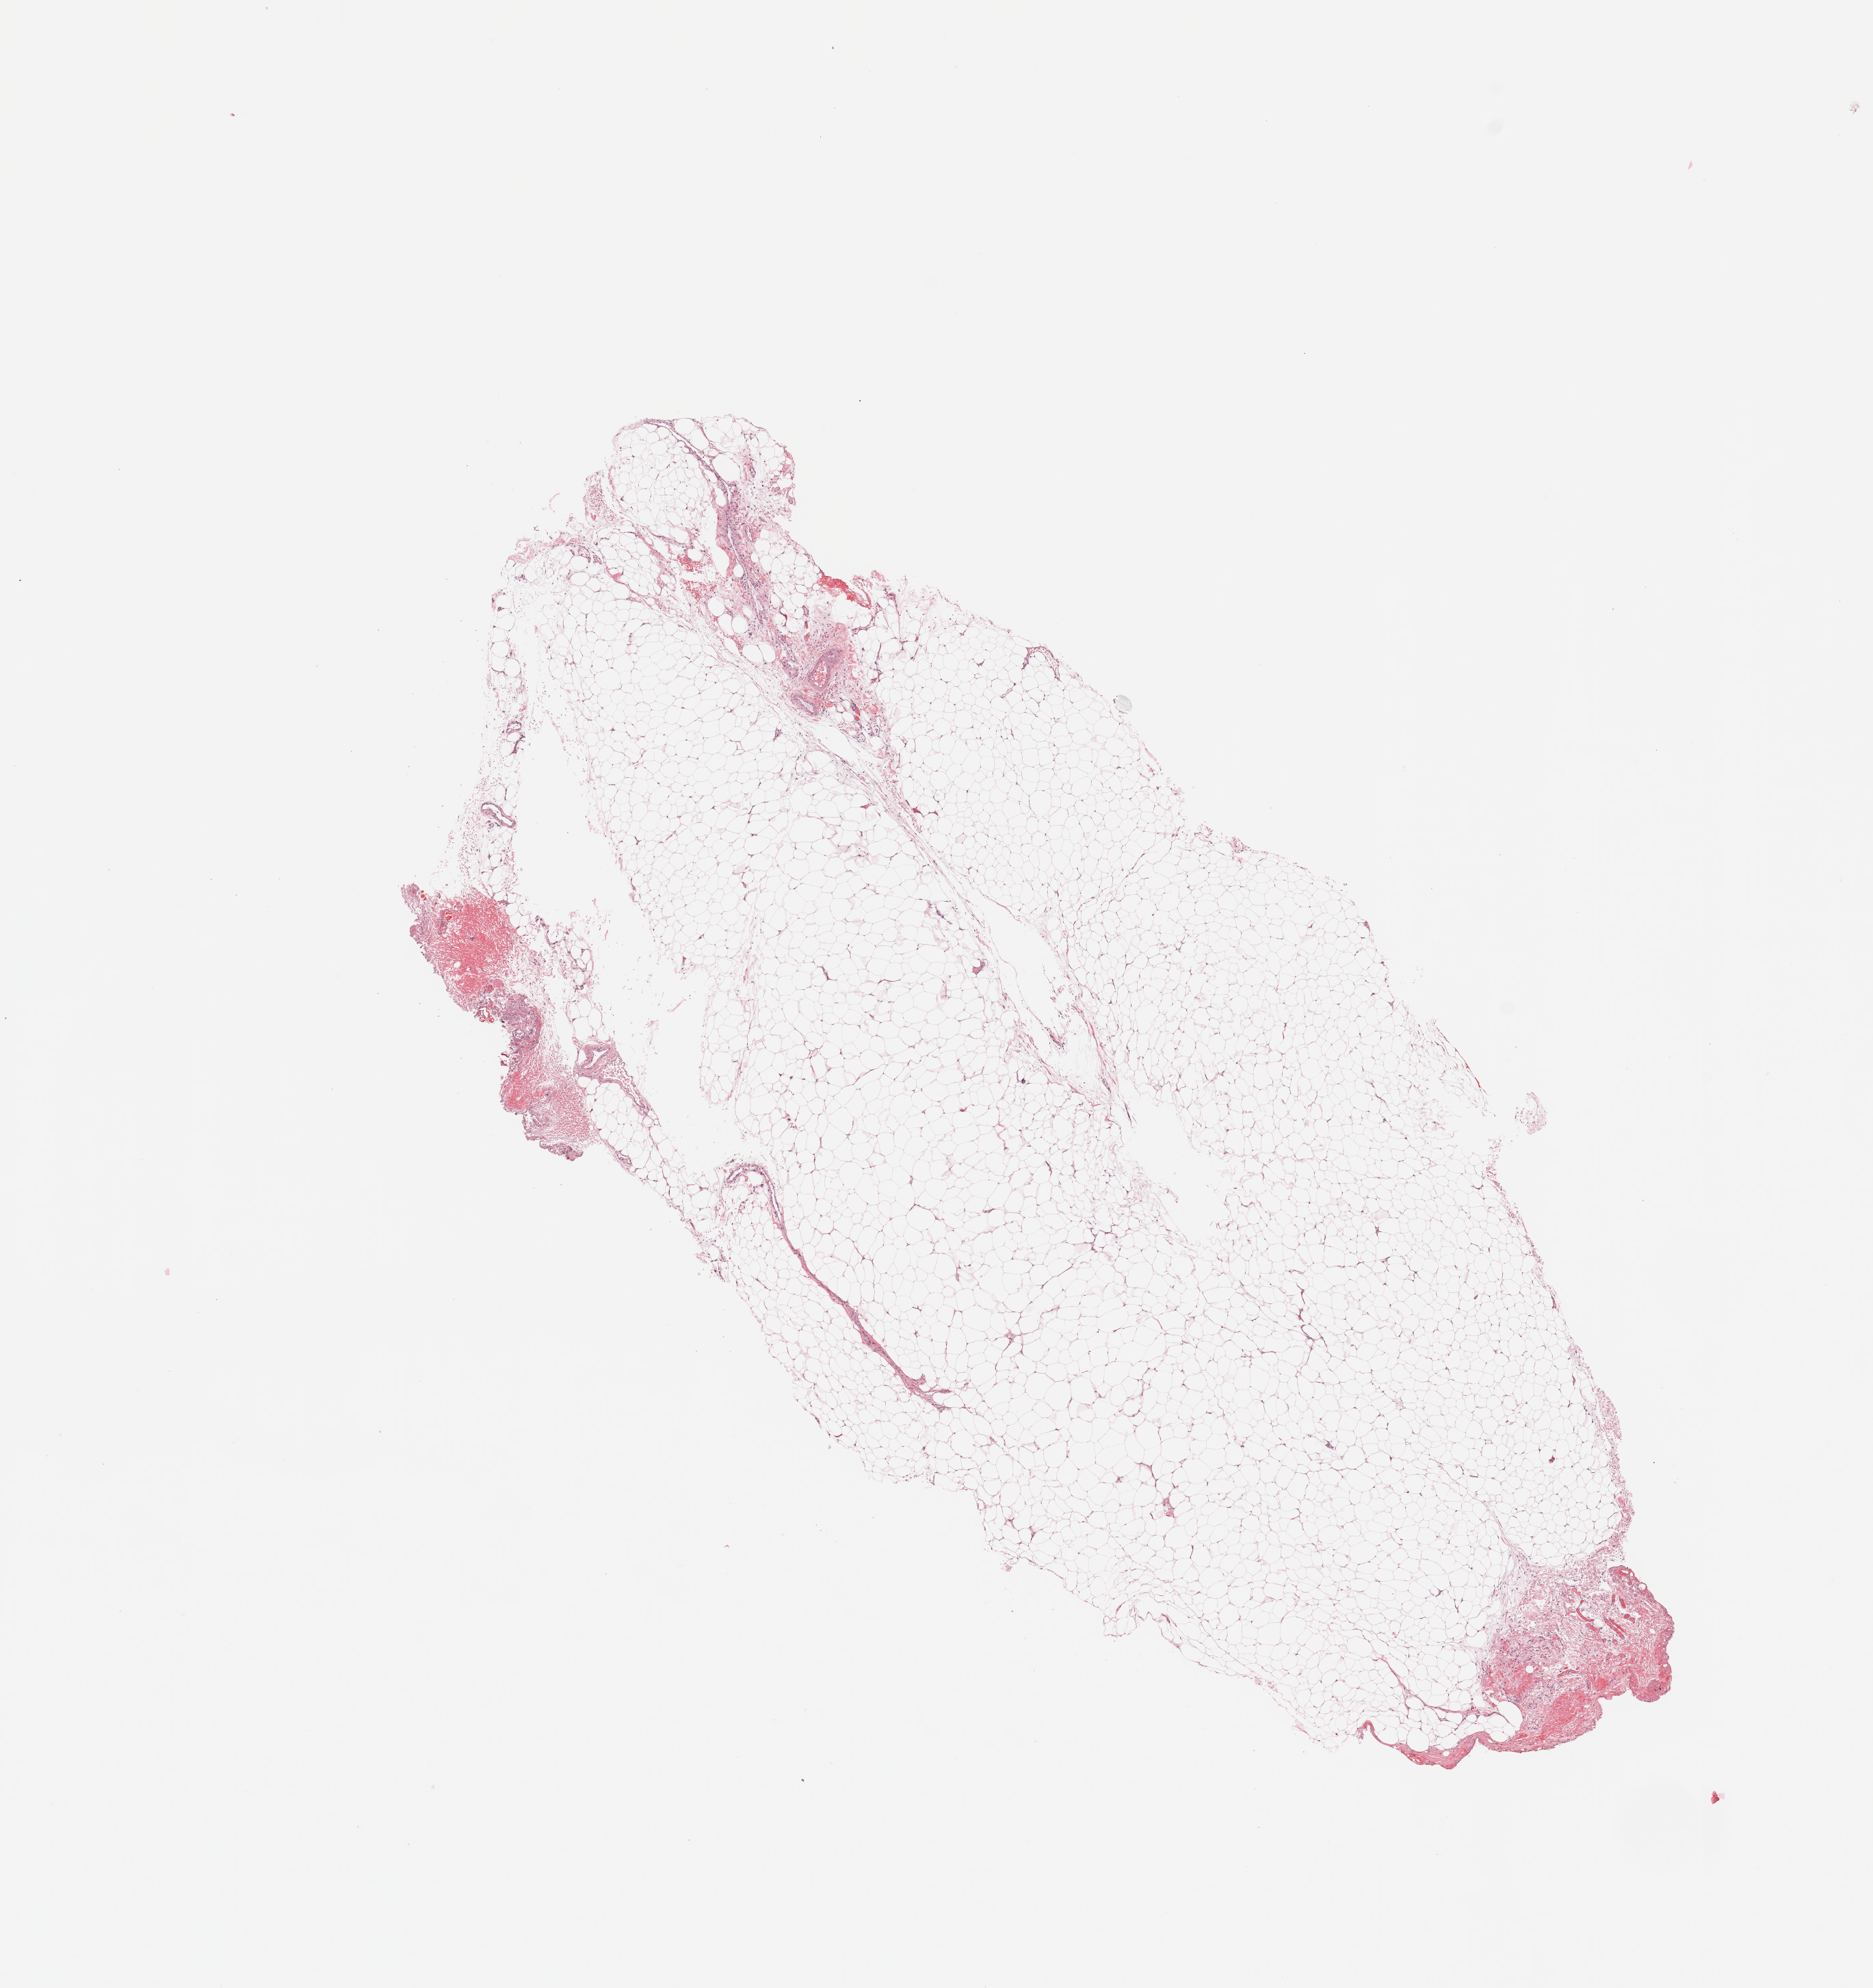
Hematoxylin and eosin (H&E) stained whole-slide image — a low-resolution overview of the entire scanned area, about 10.8 x 11.5 mm, normal (non-tumour) tissue sample, kidney. 57-year-old female patient.
This section: normal (non-tumour) tissue from the same patient. Patient diagnosis: Renal cell carcinoma, NOS.